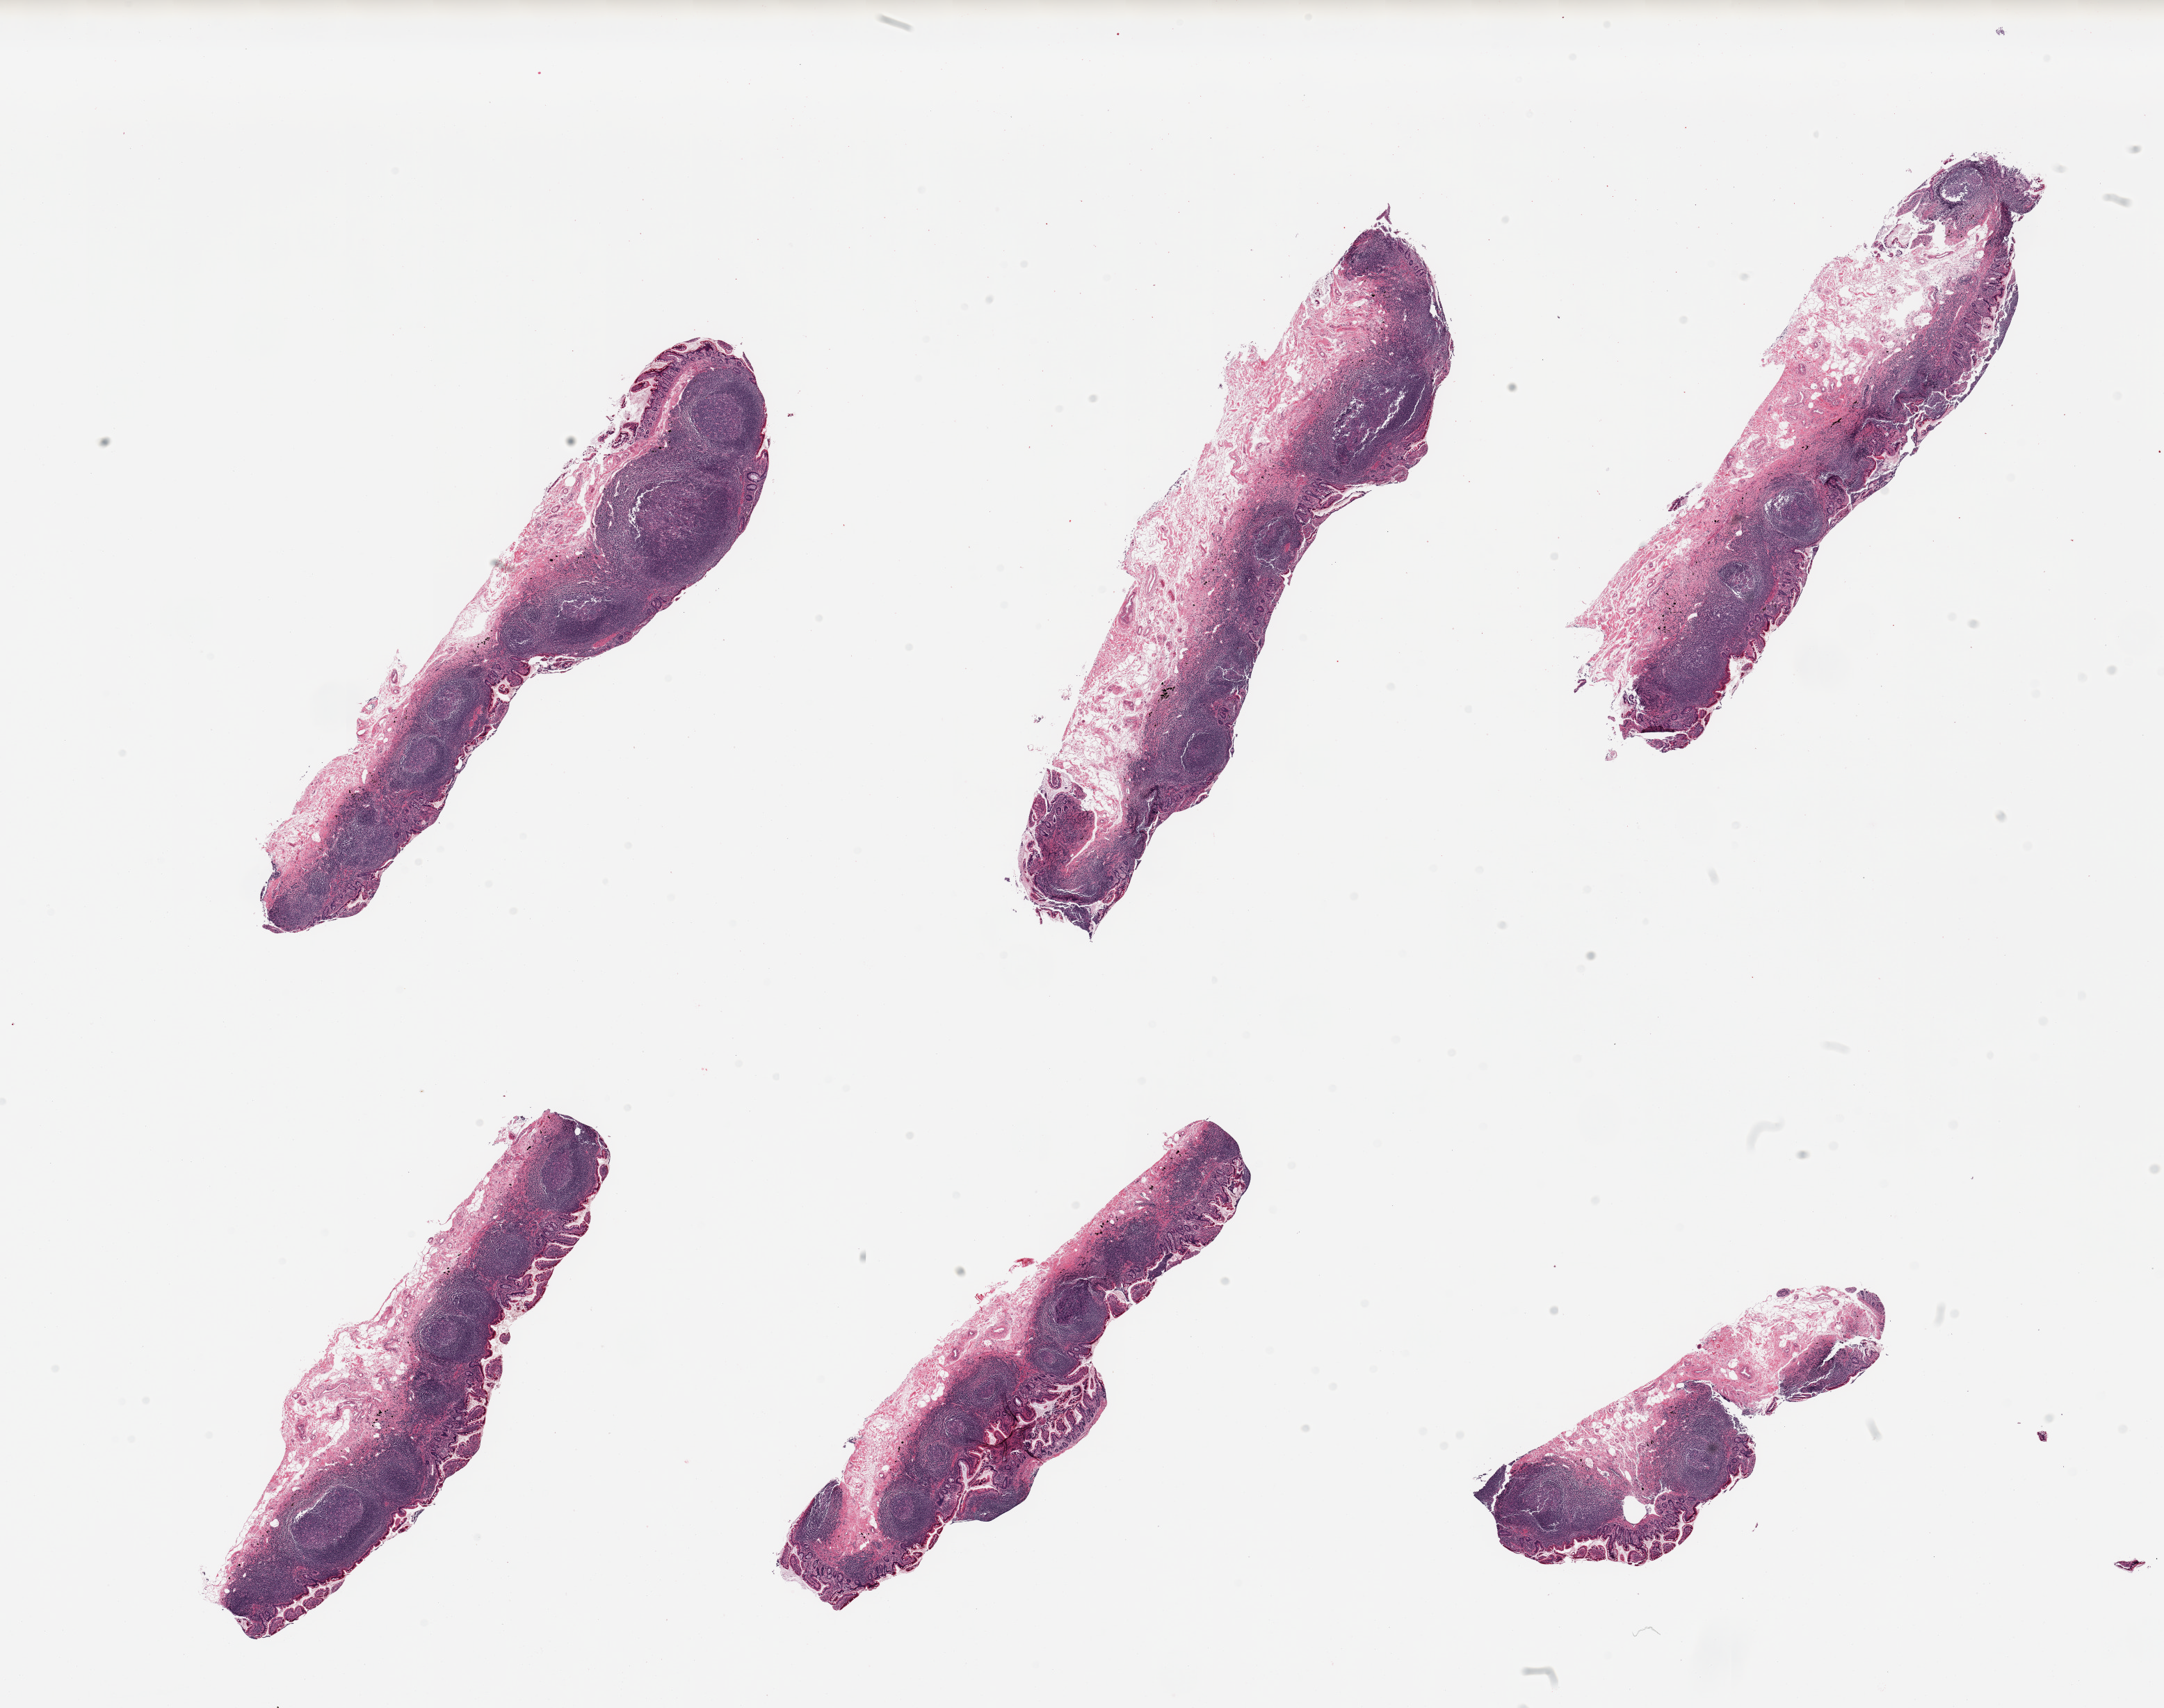
H&E whole-slide image, a low-resolution overview of the entire scanned area, about 24.6 x 19.4 mm (slide scanned at 20x), PAXgene-fixed, paraffin-embedded tissue, sampled site (target tissue): ileum, tissue donor sample. Donor: female.
Pathologist's review note for this sample: 6 pieces, well preserved, abundant lymphoid aggregates are ~60-70%, valuable specimen.